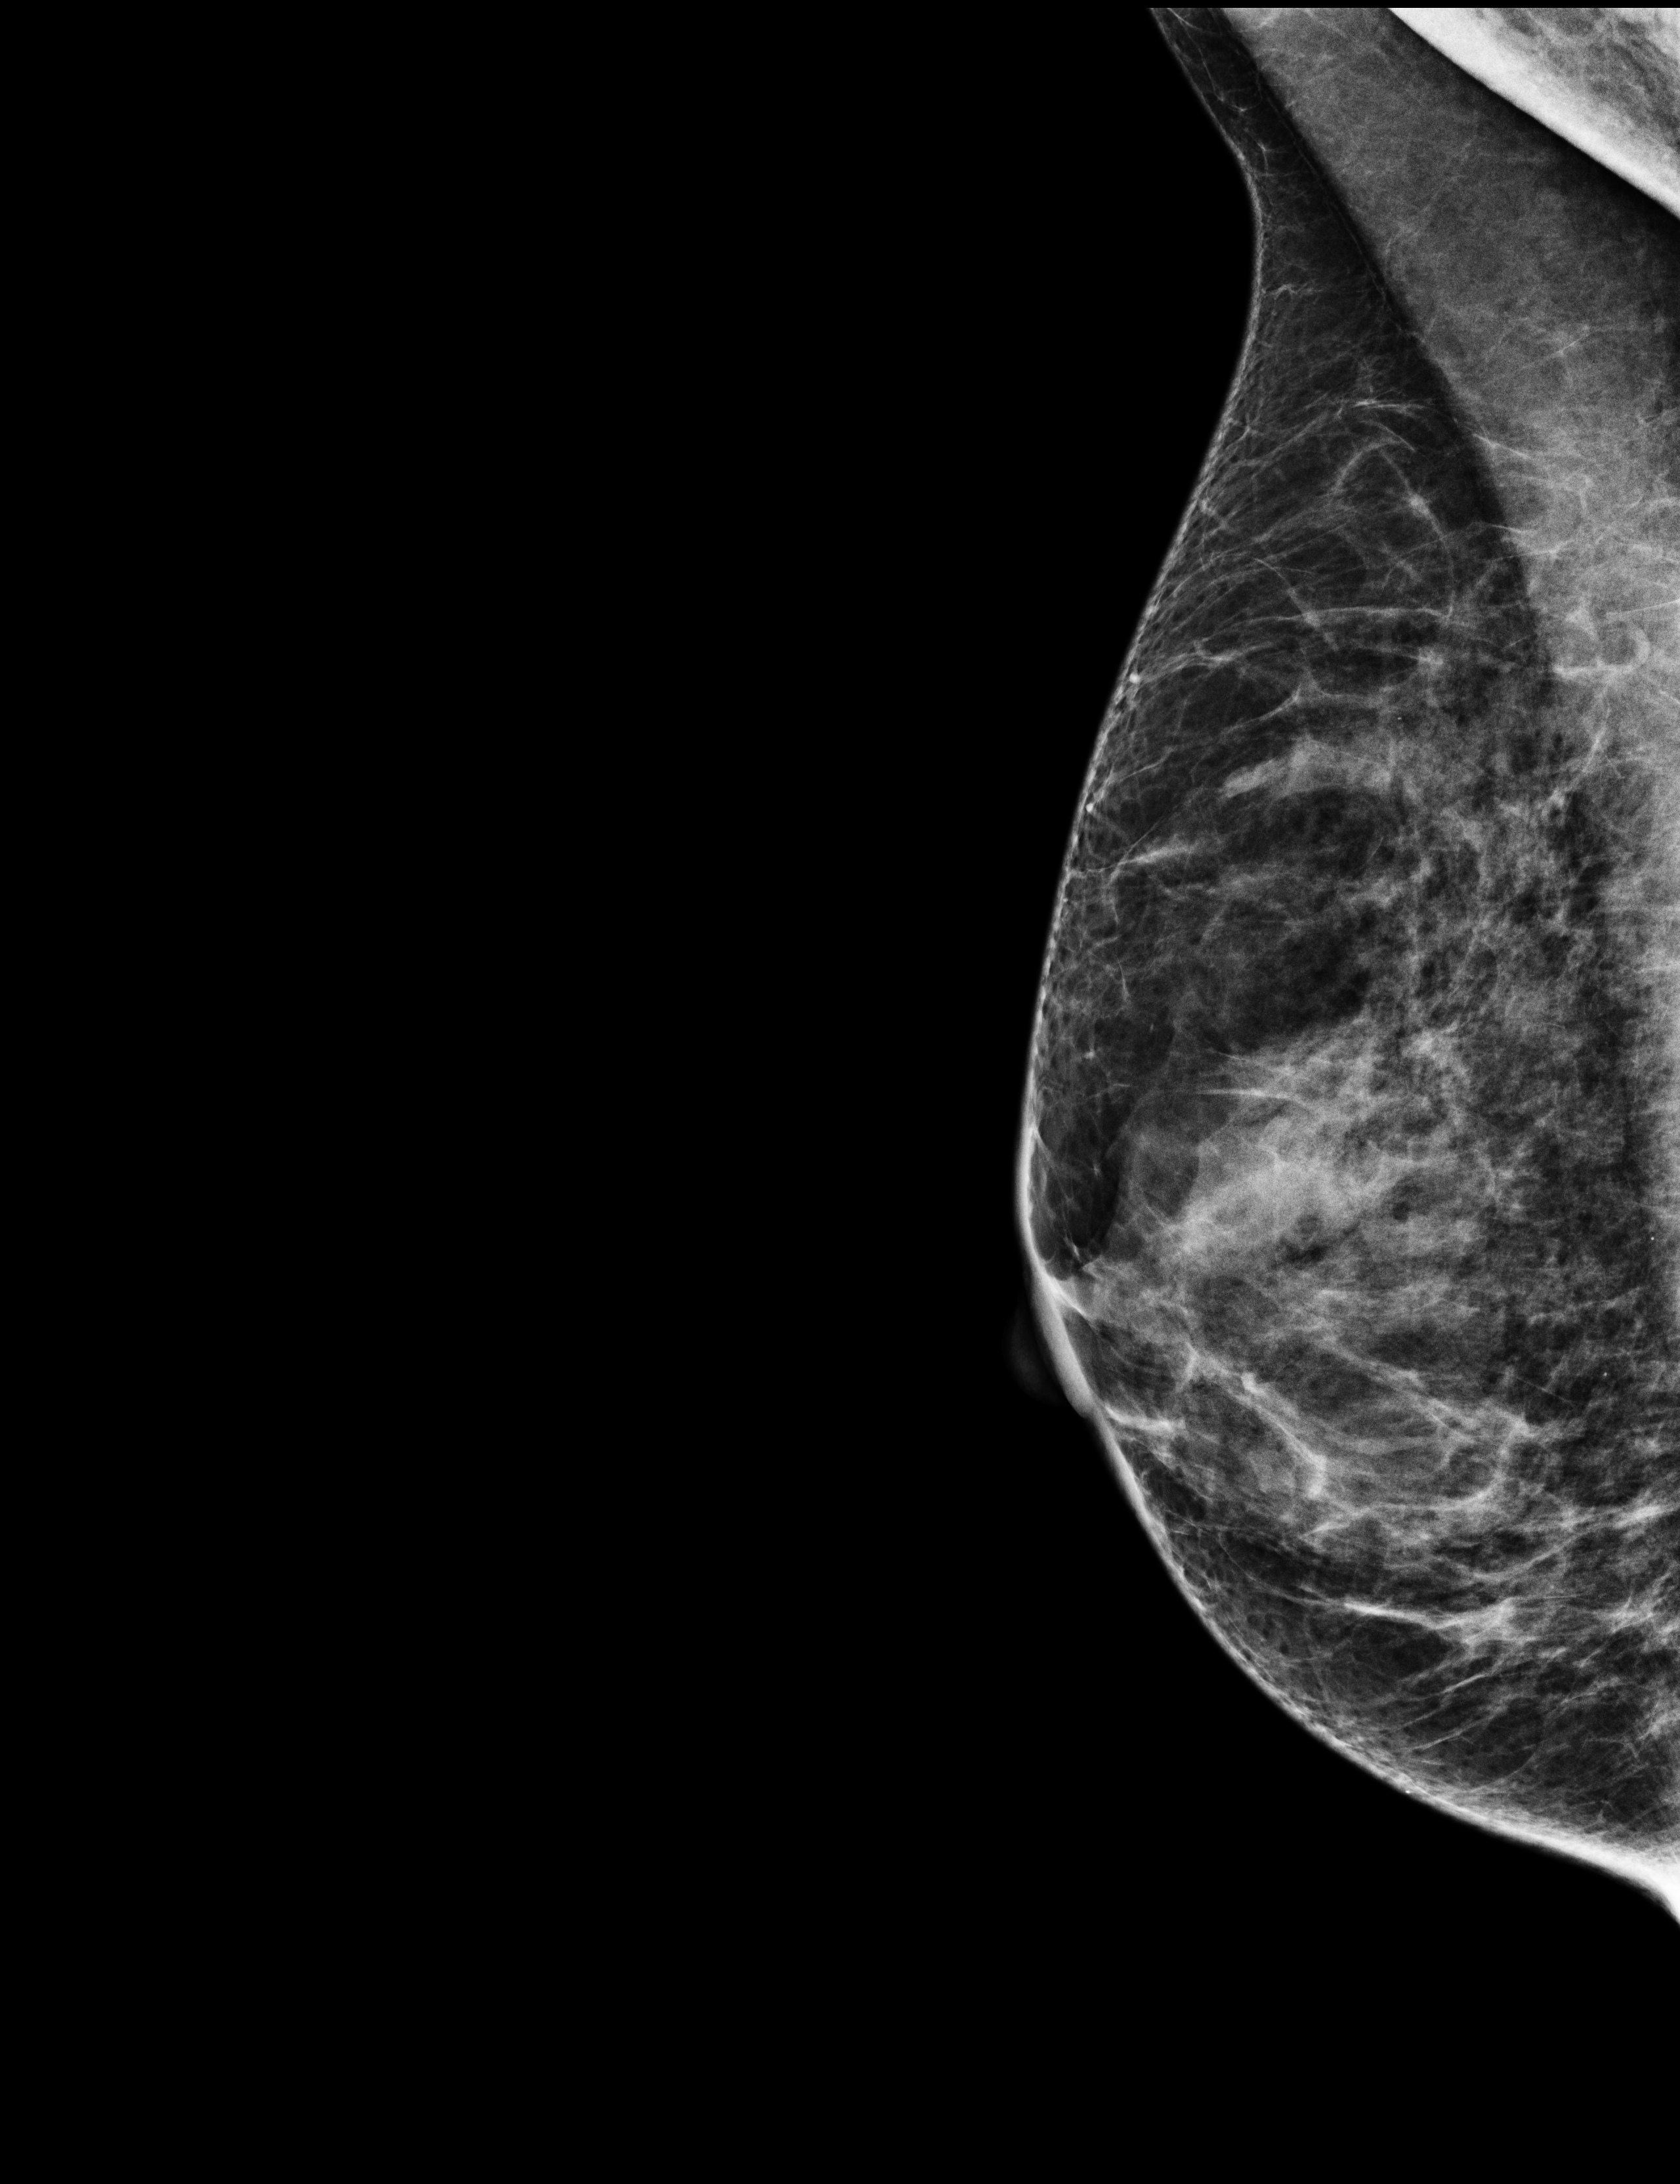
Screening examination, compressed breast thickness 55 mm. Patient: female, 56 years.
Image type: full-field digital mammogram. Breast: right. Projection: medio-lateral oblique projection.